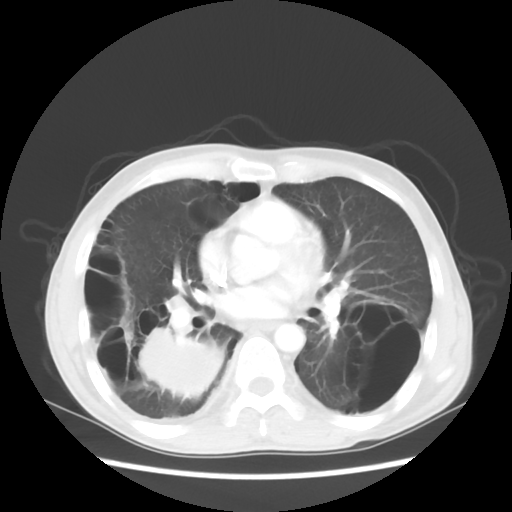
Chest CT, one axial slice; position 26 of 56 along the scan axis; 140 kVp; lung window (W 1500 / L -600 HU); 512 × 512 image matrix, field of view 351 × 351 mm. Patient: male, 41 years. From the clinical record (not read from this slice): clinical TNM (as recorded): T4 N0 M1a; histopathological grade: G3.
Outlined on this slice (rectangle marked by the reading radiologist):
- lung tumour (recorded histology: large cell carcinoma): box from (x=125, y=307) to (x=234, y=412) px